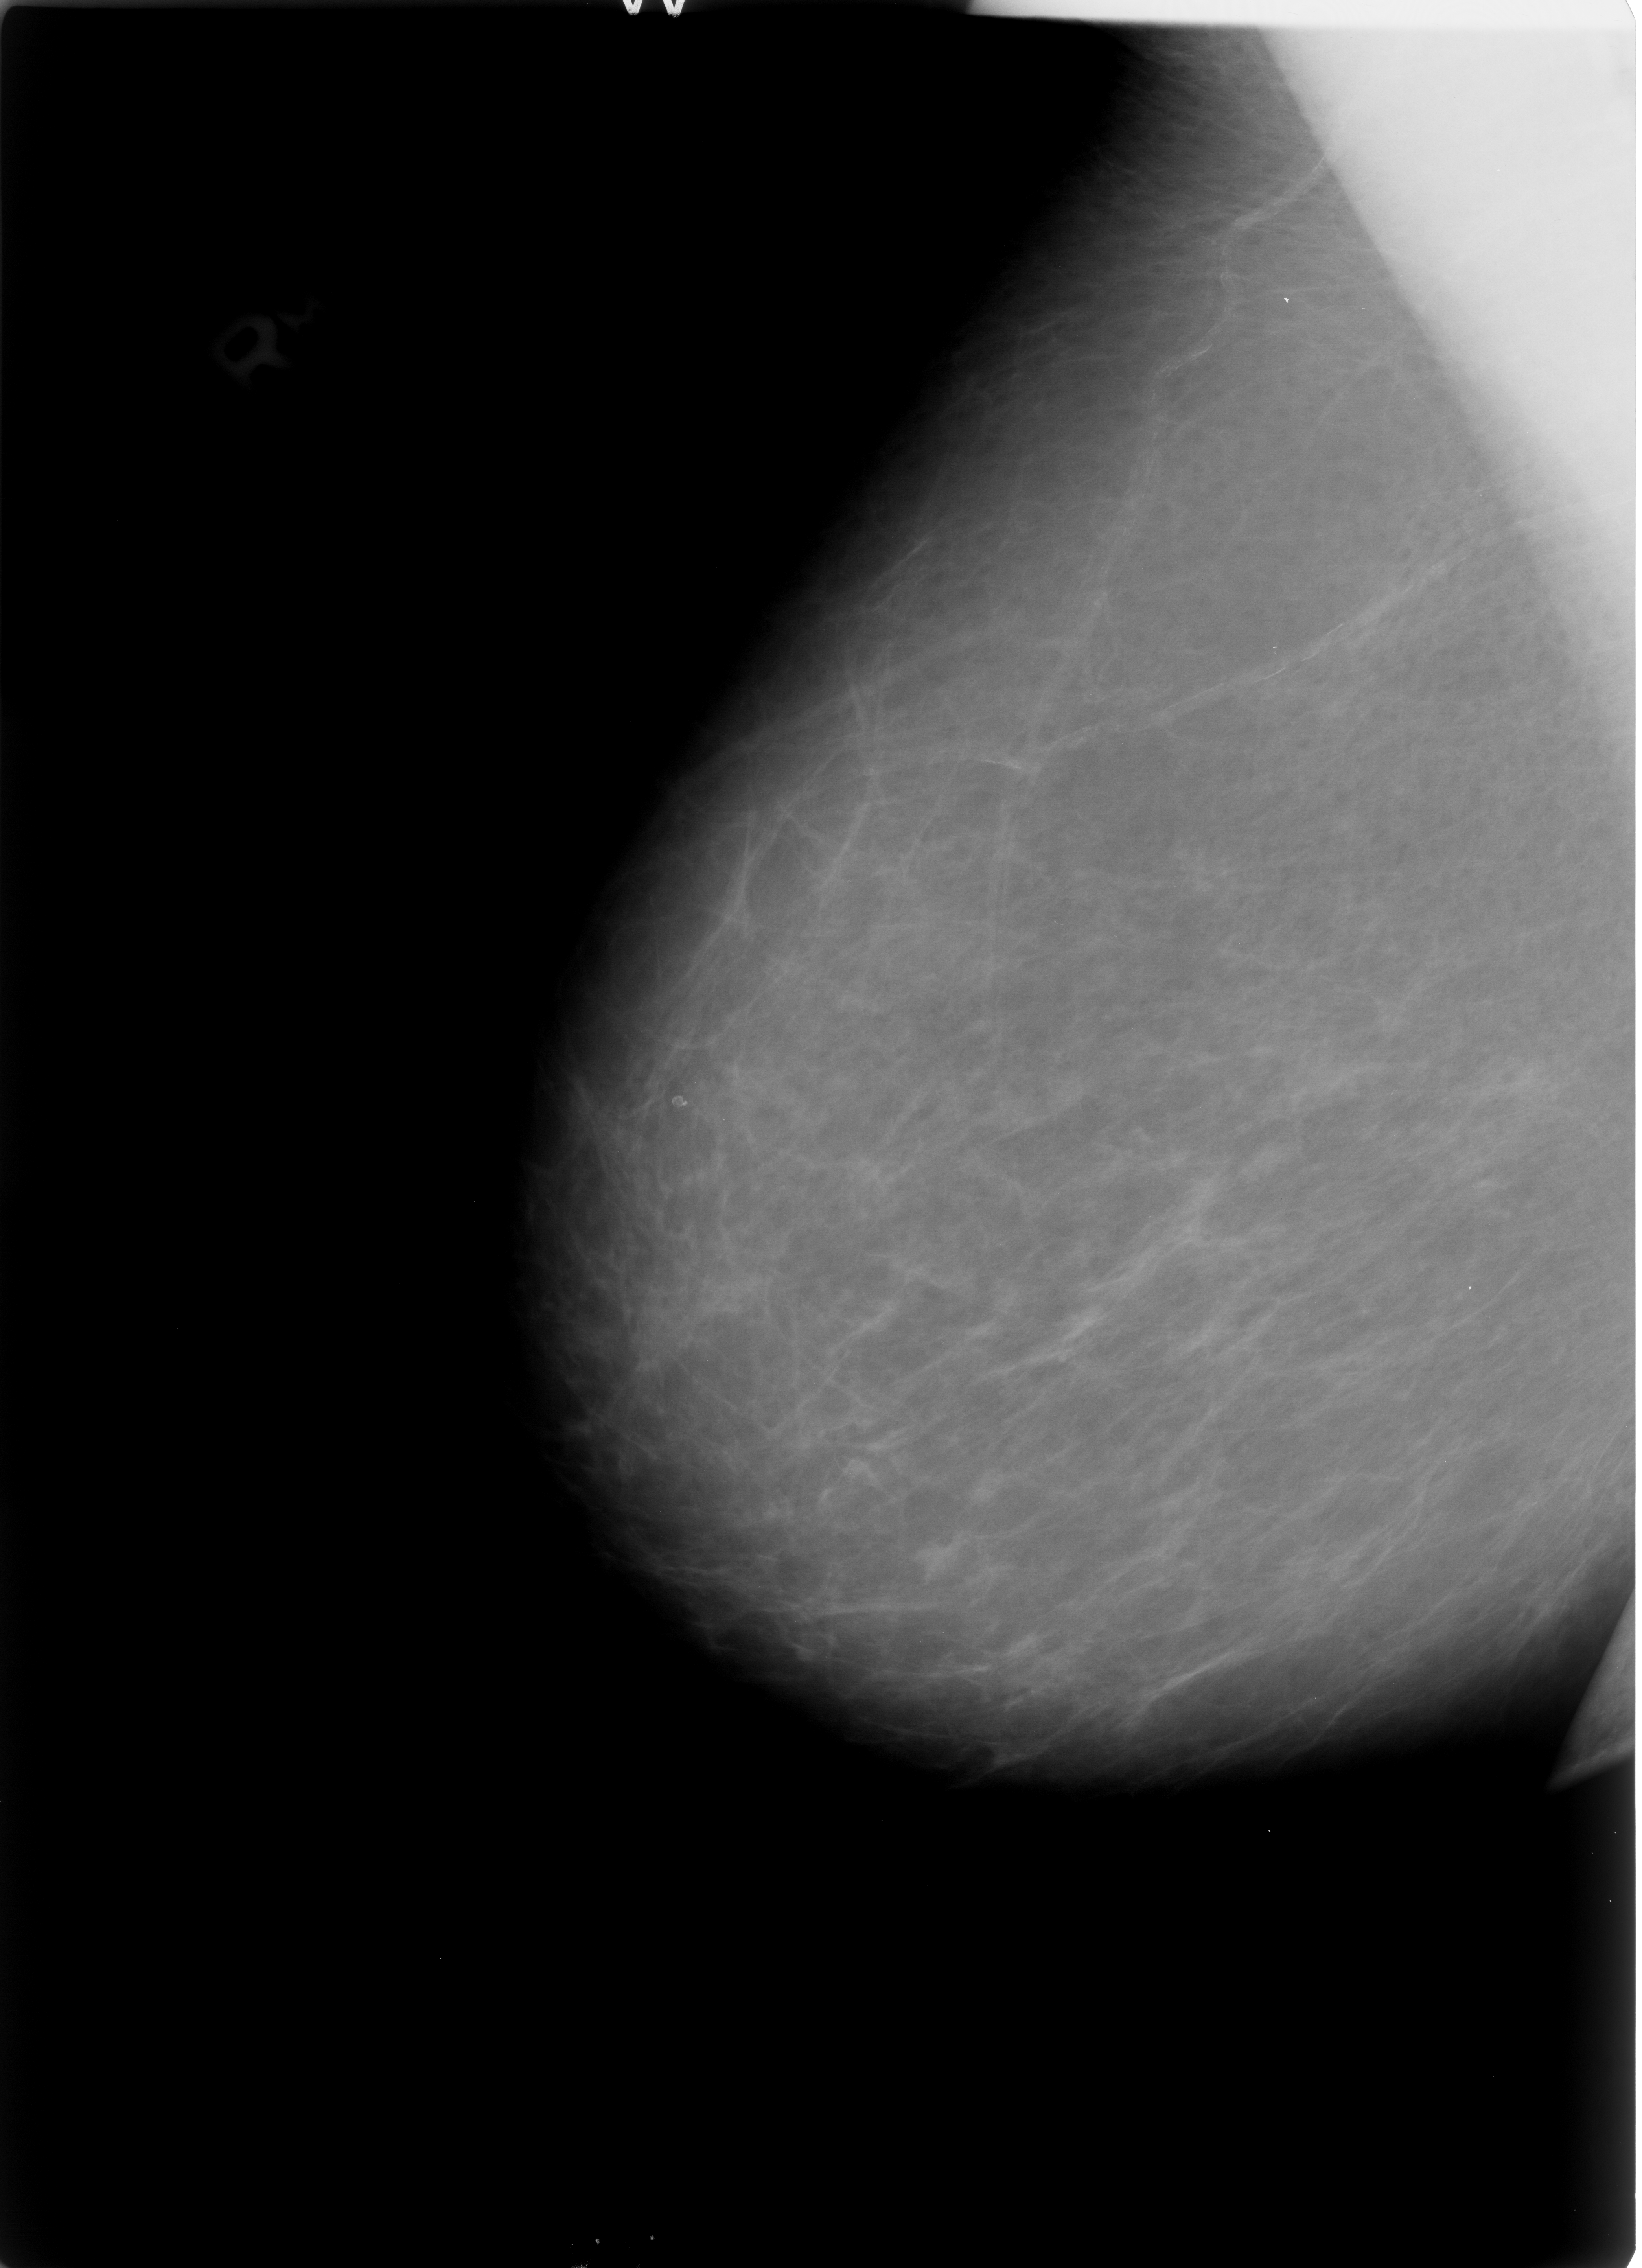
Digitized screen-film mammogram, right breast, MLO view, BI-RADS breast density category 1 (scale 1–4).
Marked findings (only marked abnormalities are described; nothing is implied about the rest of the image): calcifications, morphology lucent centered; BI-RADS assessment category 2; subtlety rating 3 on a 1 (subtle) to 5 (obvious) scale; benign without callback (not worked up further).